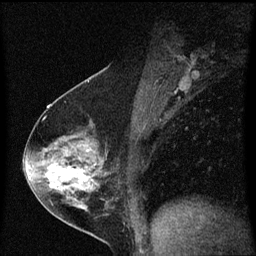
Breast MRI (dynamic contrast-enhanced), one sagittal slice. Position 33 of 60 along the scan axis. Dynamic contrast-enhanced series, image 2 of 3 at this slice position (ordered by acquisition). 1.5 T. TE 4.2 ms, TR 8.4 ms. 256 × 256 image matrix, field of view 200 × 200 mm. Patient: female, 54 years. From the clinical record (not read from this slice): setting: breast cancer imaged before/during neoadjuvant chemotherapy; receptor status: HER2-positive.
Outlined on this slice (semi-automatically segmented with operator editing):
- analysis volume of interest (the breast-tissue region the enhancement analysis was run in; not a lesion): box from (x=32, y=122) to (x=121, y=213) px
- tumour enhancement mask (voxels above the 70 % enhancement threshold inside the analysis volume of interest): (x=48, y=166)–(x=89, y=187)